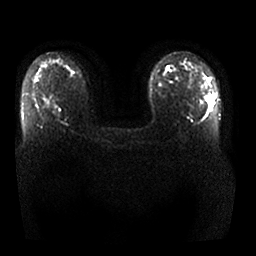
Breast MRI, one axial slice; slice 17 of 25 in the series (ordered by position); diffusion-weighted series; image 2 of 4 stored at this slice position (different b-values; order by instance number); 1.5 T; 256 × 256 image matrix, field of view 360 × 360 mm. Female patient.
Structures marked on this image (outlined manually by an expert reader):
- tumour on diffusion-weighted imaging: bounding box <206,96,214,104> (left, top, right, bottom; pixels)